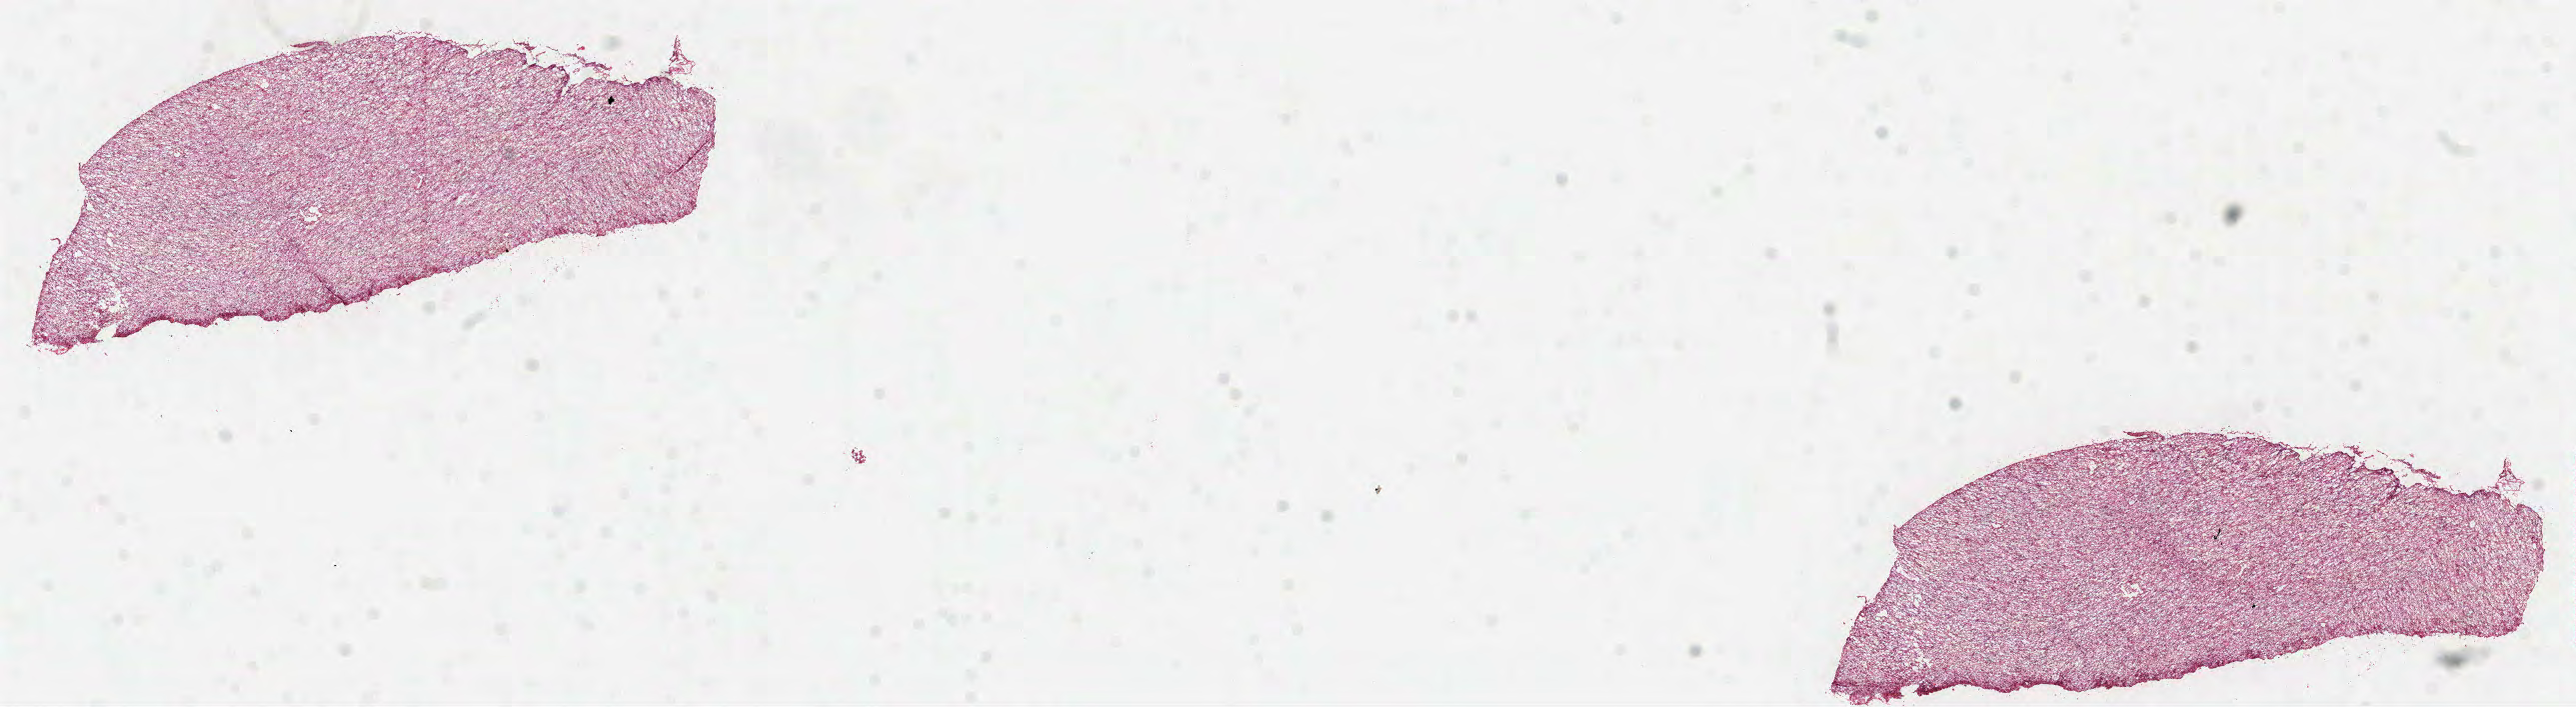
Hematoxylin and eosin (H&E) stained whole-slide image, whole scanned area (about 20.8 x 5.7 mm) shown as a low-resolution overview, FFPE section, brain, primary tumour sample. Male patient; age at initial diagnosis 70 years.
Diagnosis: Glioblastoma.